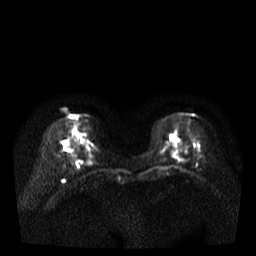
Breast MRI, one axial slice; position 12 of 35 along the scan axis; diffusion-weighted series; image 2 of 4 stored at this slice position (different b-values; order by instance number); 3 T; 5 mm slice thickness; 256 × 256 image matrix, field of view 320 × 320 mm. Female patient.
Annotated regions visible in this slice (outlined manually by an expert reader):
- tumour on diffusion-weighted imaging: bounding box <173,154,181,161> (left, top, right, bottom; pixels)